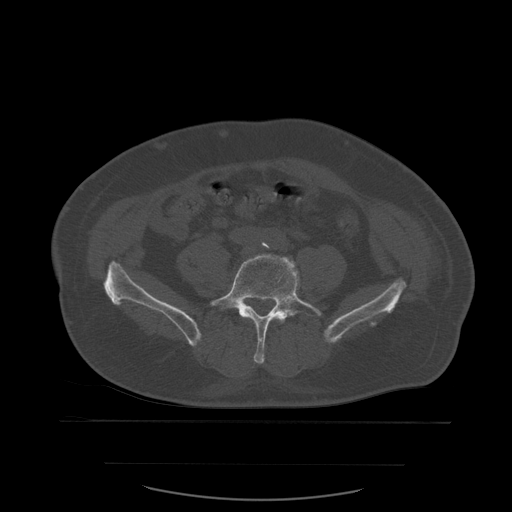
CT including the spine, one axial slice. Slice 141 of 590 in the series (ordered by position). Bone window (W 1800 / L 400 HU). 512 × 512 image matrix, field of view 479 × 479 mm. Patient age 71 years. From the clinical record (not read from this slice): primary cancer: lung.
Annotated regions visible in this slice (semi-automatic segmentation, software-assisted and operator-edited):
- L5 vertebra: bounding box (x1, y1, x2, y2) in pixels: (210, 254, 322, 364)